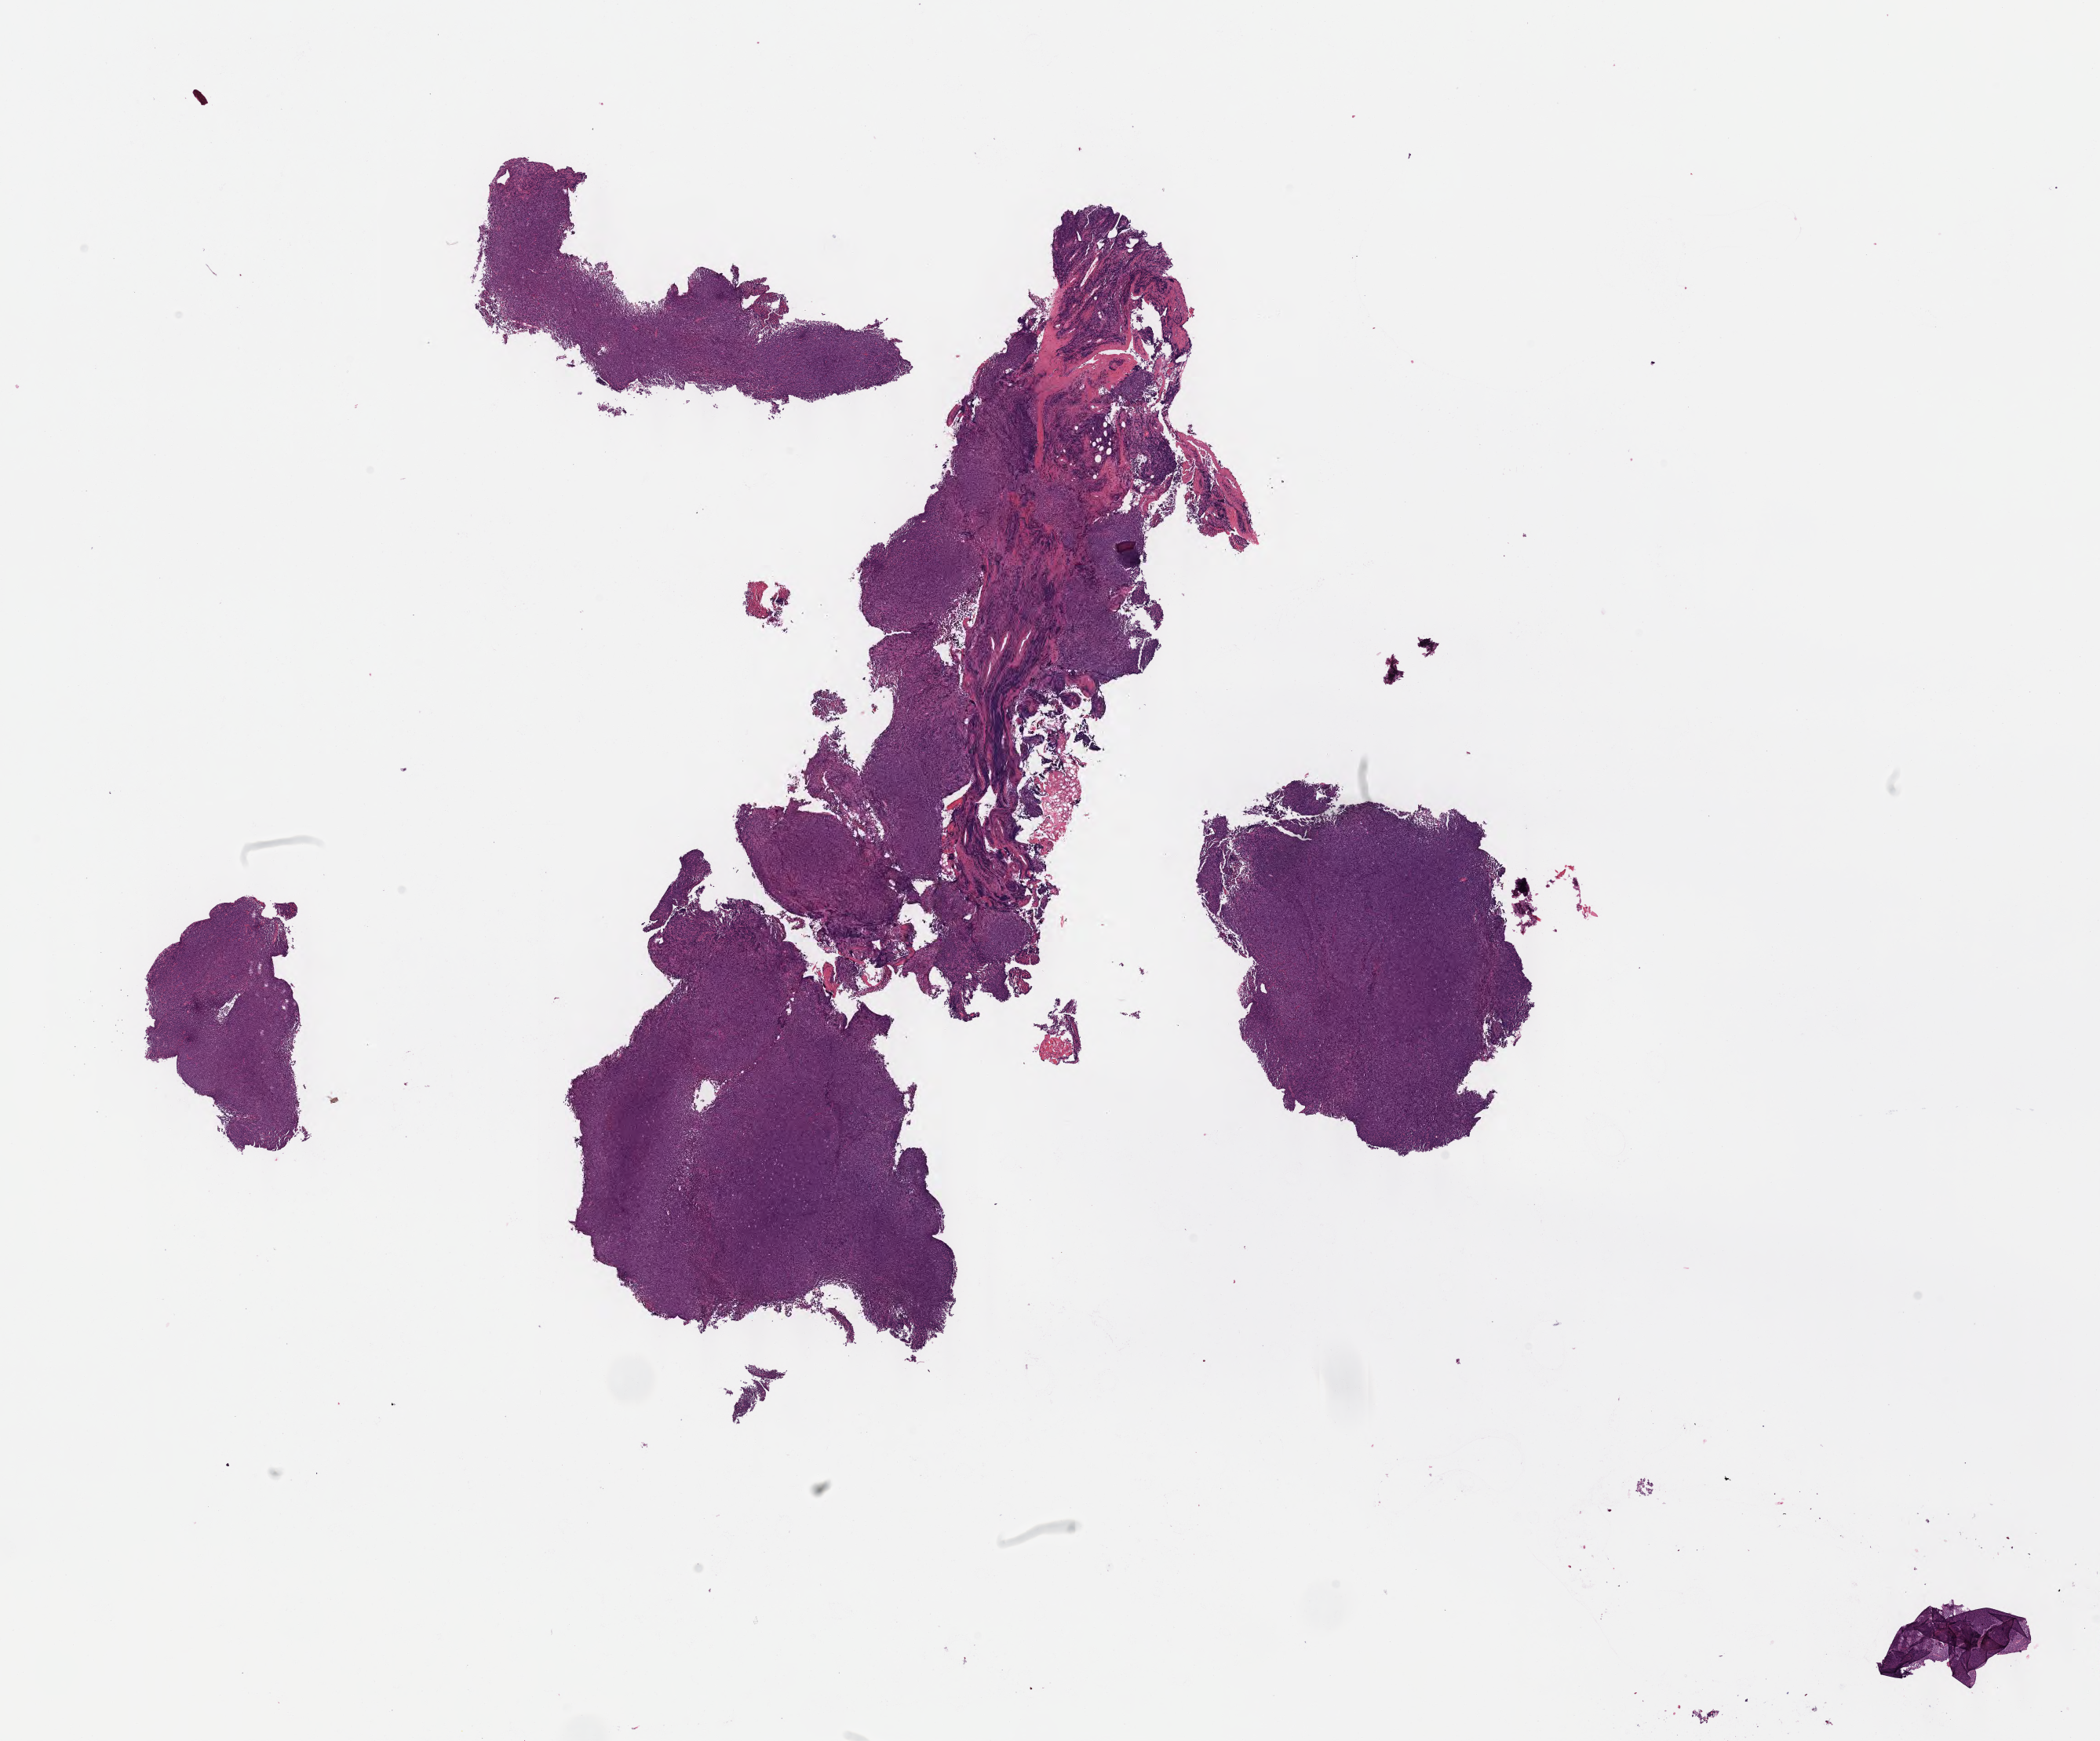
Whole-slide image, haematoxylin and eosin stain, a low-resolution overview of the entire scanned area, about 21.6 x 17.9 mm; tumor tissue; site: liver. Female patient, 36 years old.
Diagnosis: Diffuse large B-cell lymphoma, NOS.